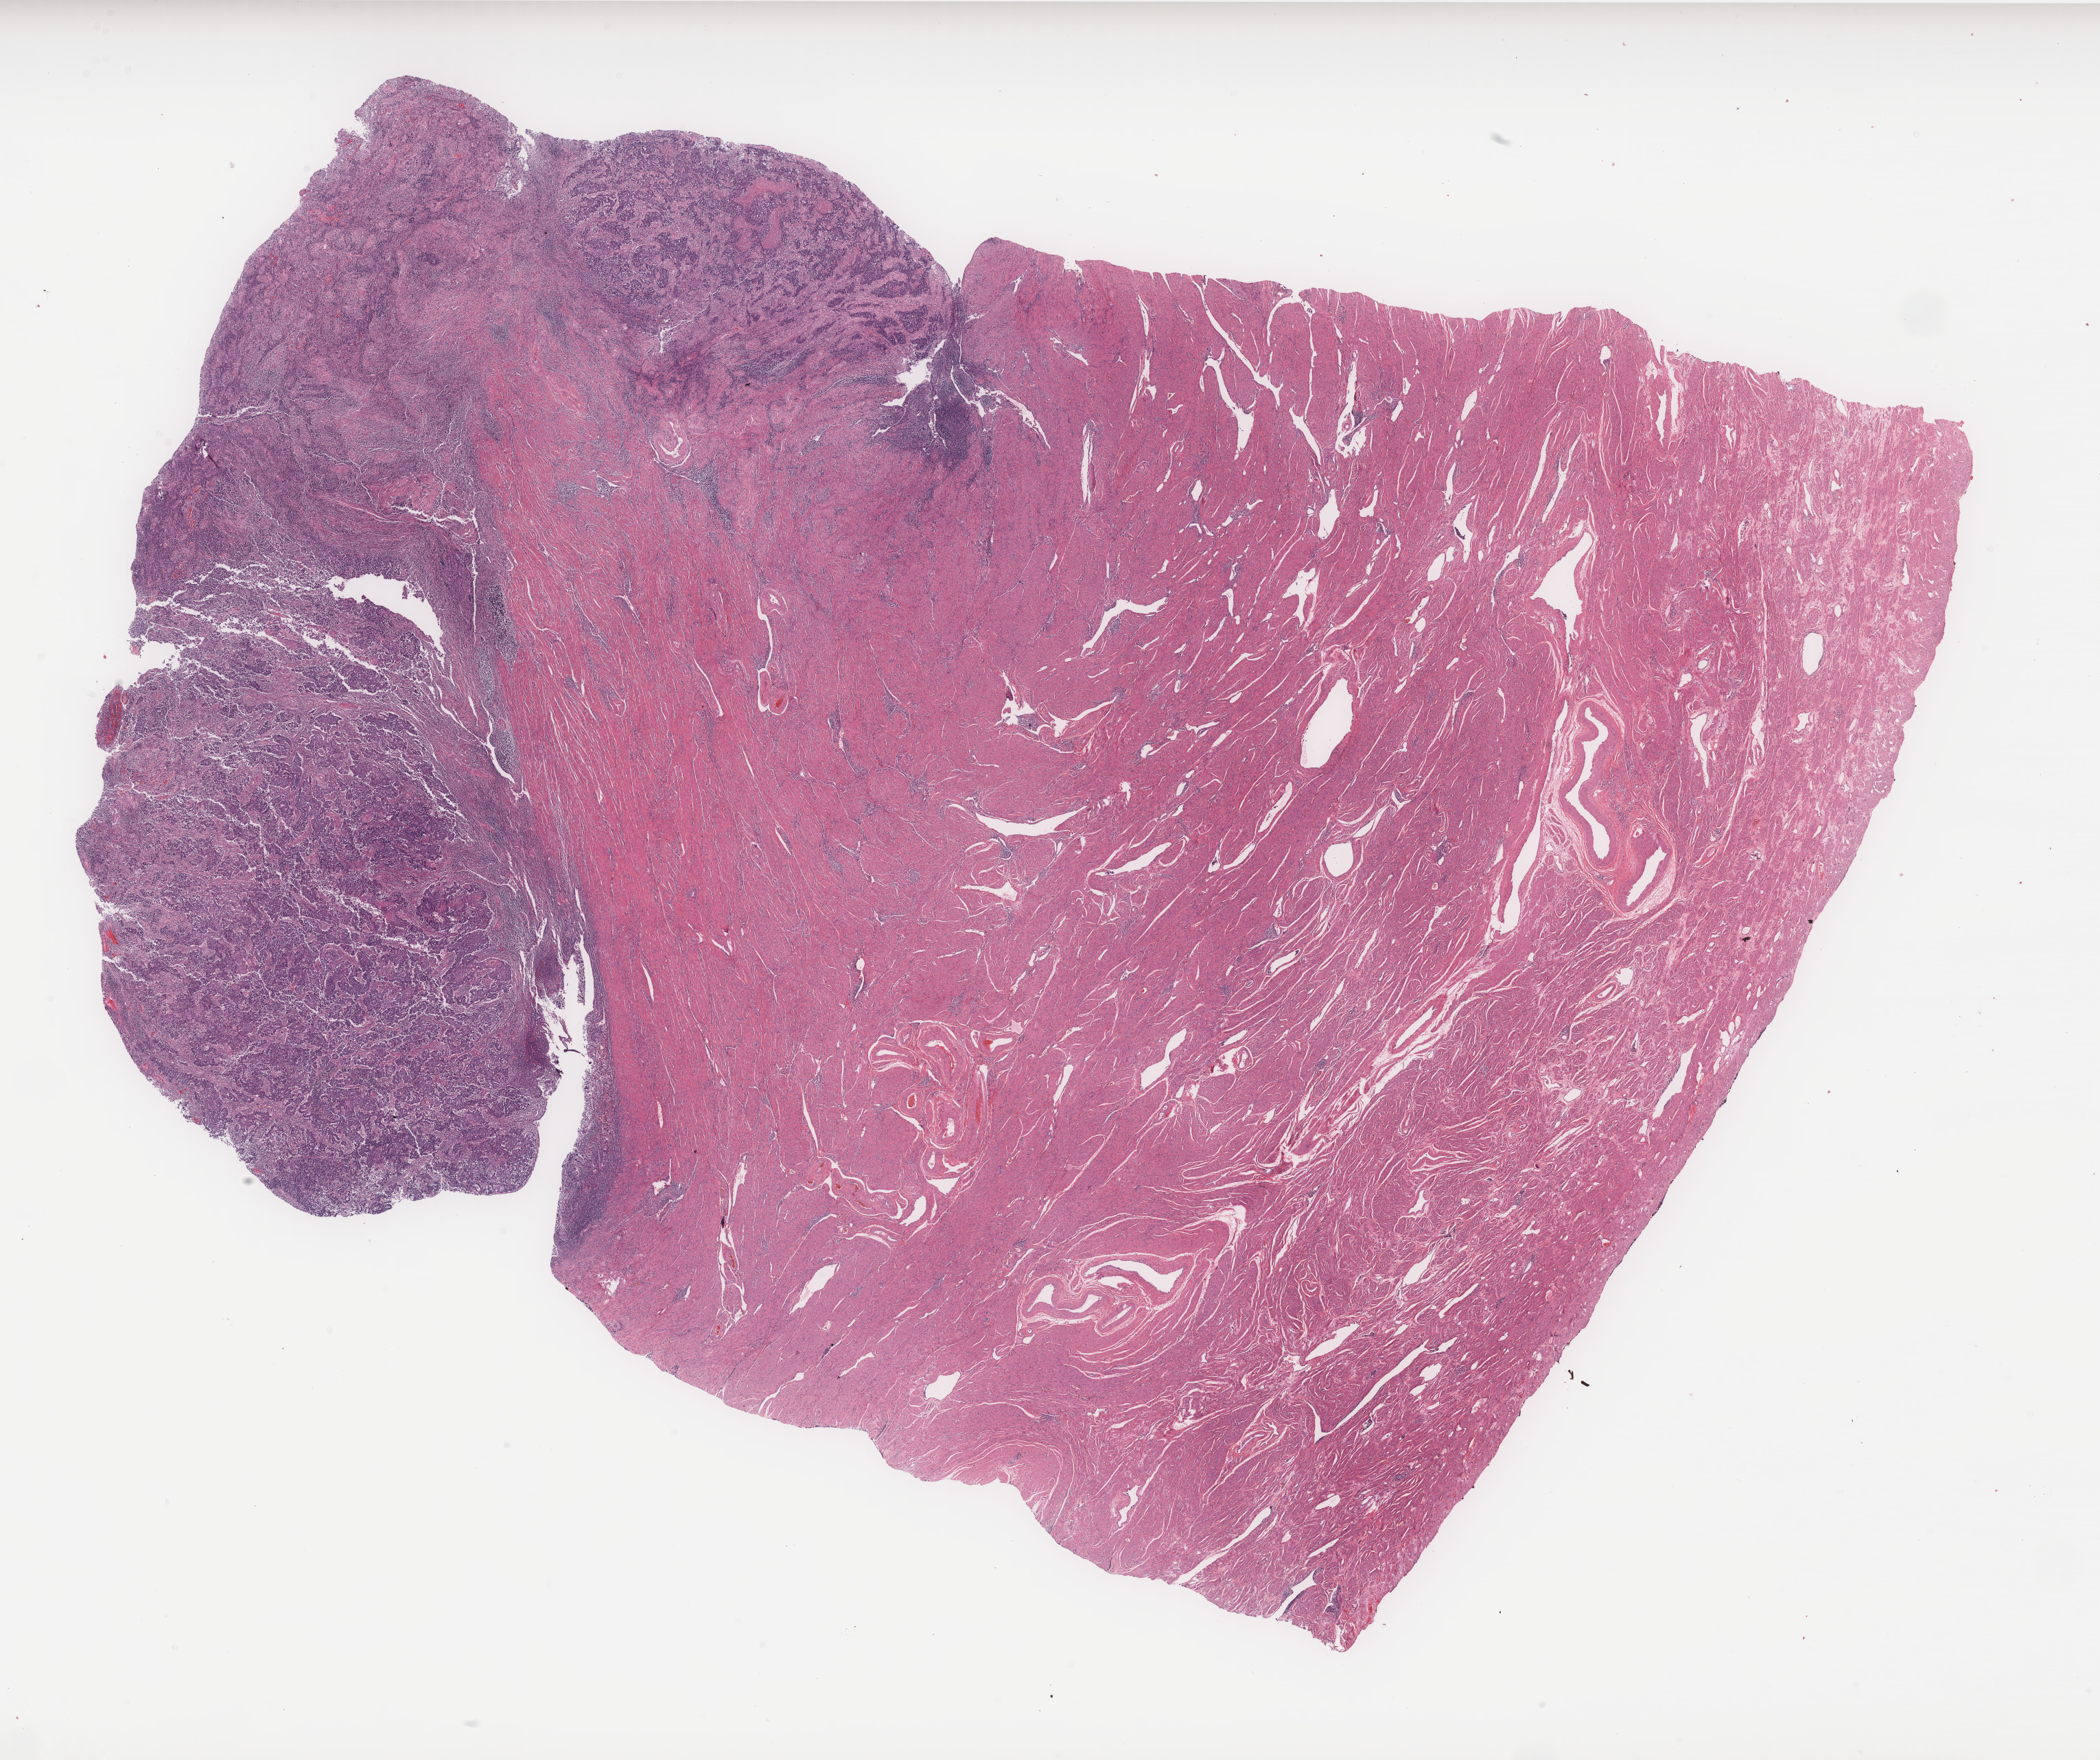
Digitized Hematoxylin and eosin (H&E) stained tissue section (whole slide) — shown as a low-resolution overview of the whole scanned area (about 24.5 x 20.6 mm, slide scanned at 40x). Formalin-fixed paraffin-embedded (FFPE) diagnostic section. Primary tumour sample from the uterus. Female patient; age at initial diagnosis 46 years. Histologic grade: G3 (poorly differentiated).
Lymph nodes positive (case pathology): 0 of 4 examined. Histologic diagnosis: Endometrioid adenocarcinoma, NOS (endometrium). FIGO stage: IA.